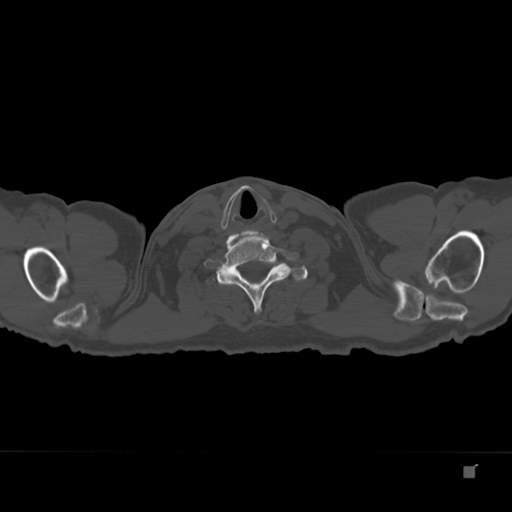
CT including the spine, one axial slice. Slice 326 of 332 in the series (ordered by position). Reconstruction kernel Br40s. Bone window (W 1800 / L 400 HU). 1.5 mm slice thickness. 512 × 512 image matrix, field of view 389 × 389 mm. Patient: male, 72 years. Case-level facts recorded for this patient, not image findings: primary cancer: skeletal.
Annotated regions visible in this slice (semi-automatically segmented with operator editing):
- T1 vertebra: bounding box [x1, y1, x2, y2] px = [206, 263, 308, 288]